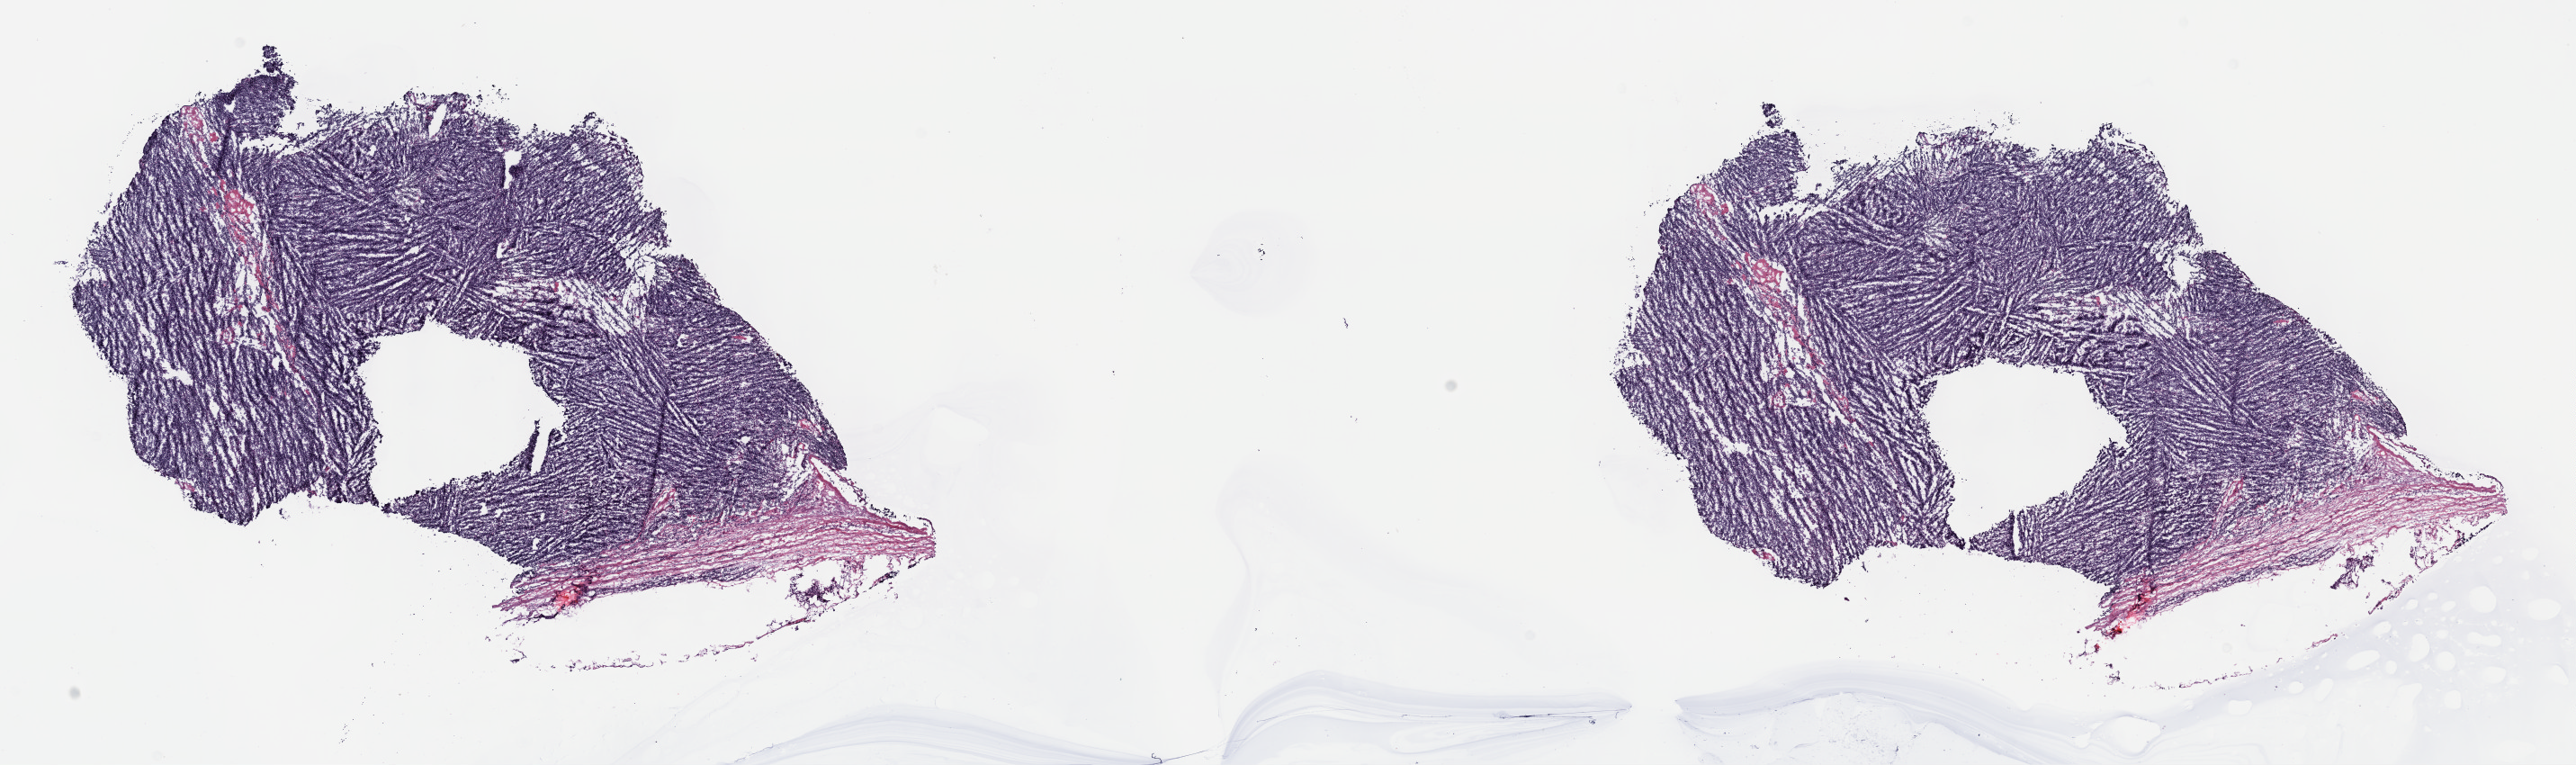
Digitized H&E tissue section (whole slide), shown as a low-resolution overview of the whole scanned area (about 23.2 x 6.9 mm); frozen section from the top of the tissue portion; thymus, primary tumour sample. Male patient; age at initial diagnosis 71 years.
Diagnosis: Thymoma, type B2, malignant.